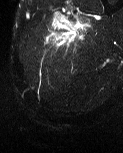
MRI of an extremity soft-tissue mass, one axial slice. Position 9 of 60 along the scan axis. T2-weighted fat-saturated. MR volume resampled by the dataset authors to the PET/CT grid (not the native acquisition matrix). 123 × 153 image matrix. Male patient. Case-level facts recorded for this patient, not image findings: histological type: pleiomorphic liposarcoma; grade: high; site of the primary tumour: left thigh.
Structures marked on this image (expert contour drawn on MRI and transferred to this co-registered scan by the dataset authors):
- gross tumour volume including surrounding oedema: bounding box (x1, y1, x2, y2) in pixels: (49, 11, 92, 44)